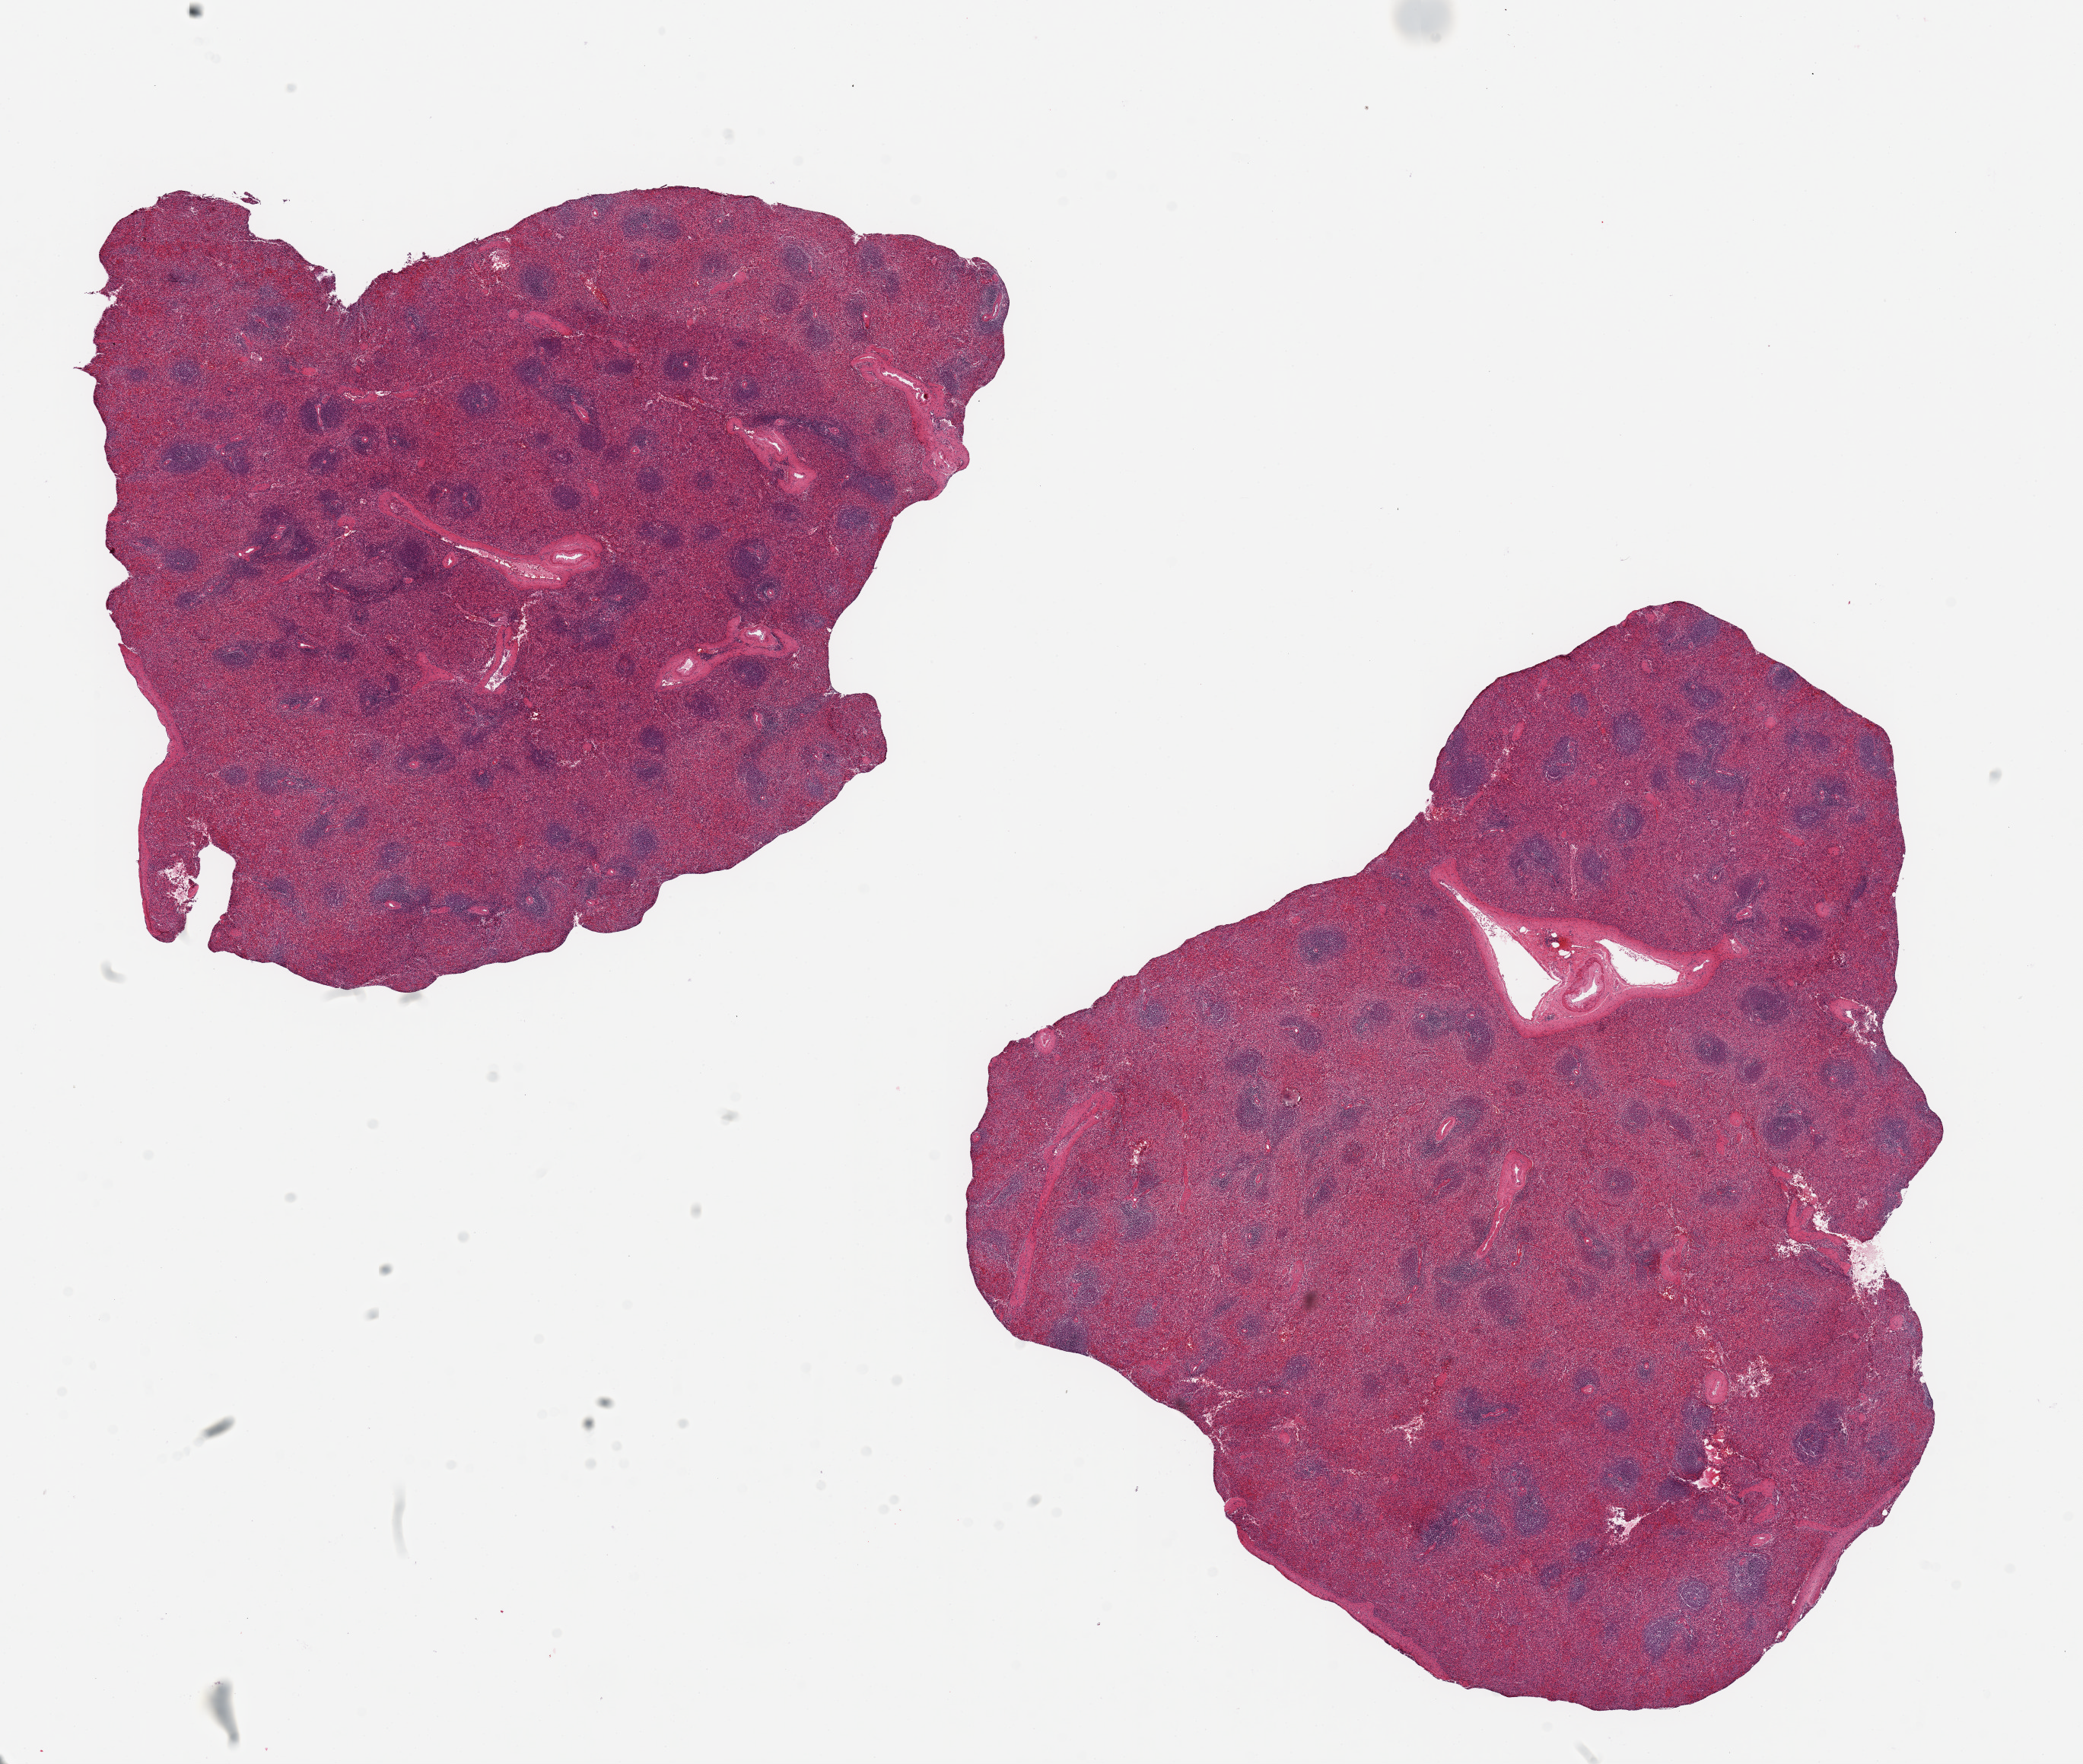
Hematoxylin and eosin (H&E) whole-slide image, shown as a low-resolution overview of the whole scanned area (about 21.7 x 18.3 mm, slide scanned at 20x). PAXgene-fixed, paraffin-embedded tissue. Target tissue: spleen. Donor tissue sample. Donor sex: female.
Reviewer comment on this tissue sample: 2 pieces, 10x8 & 11x10mm.